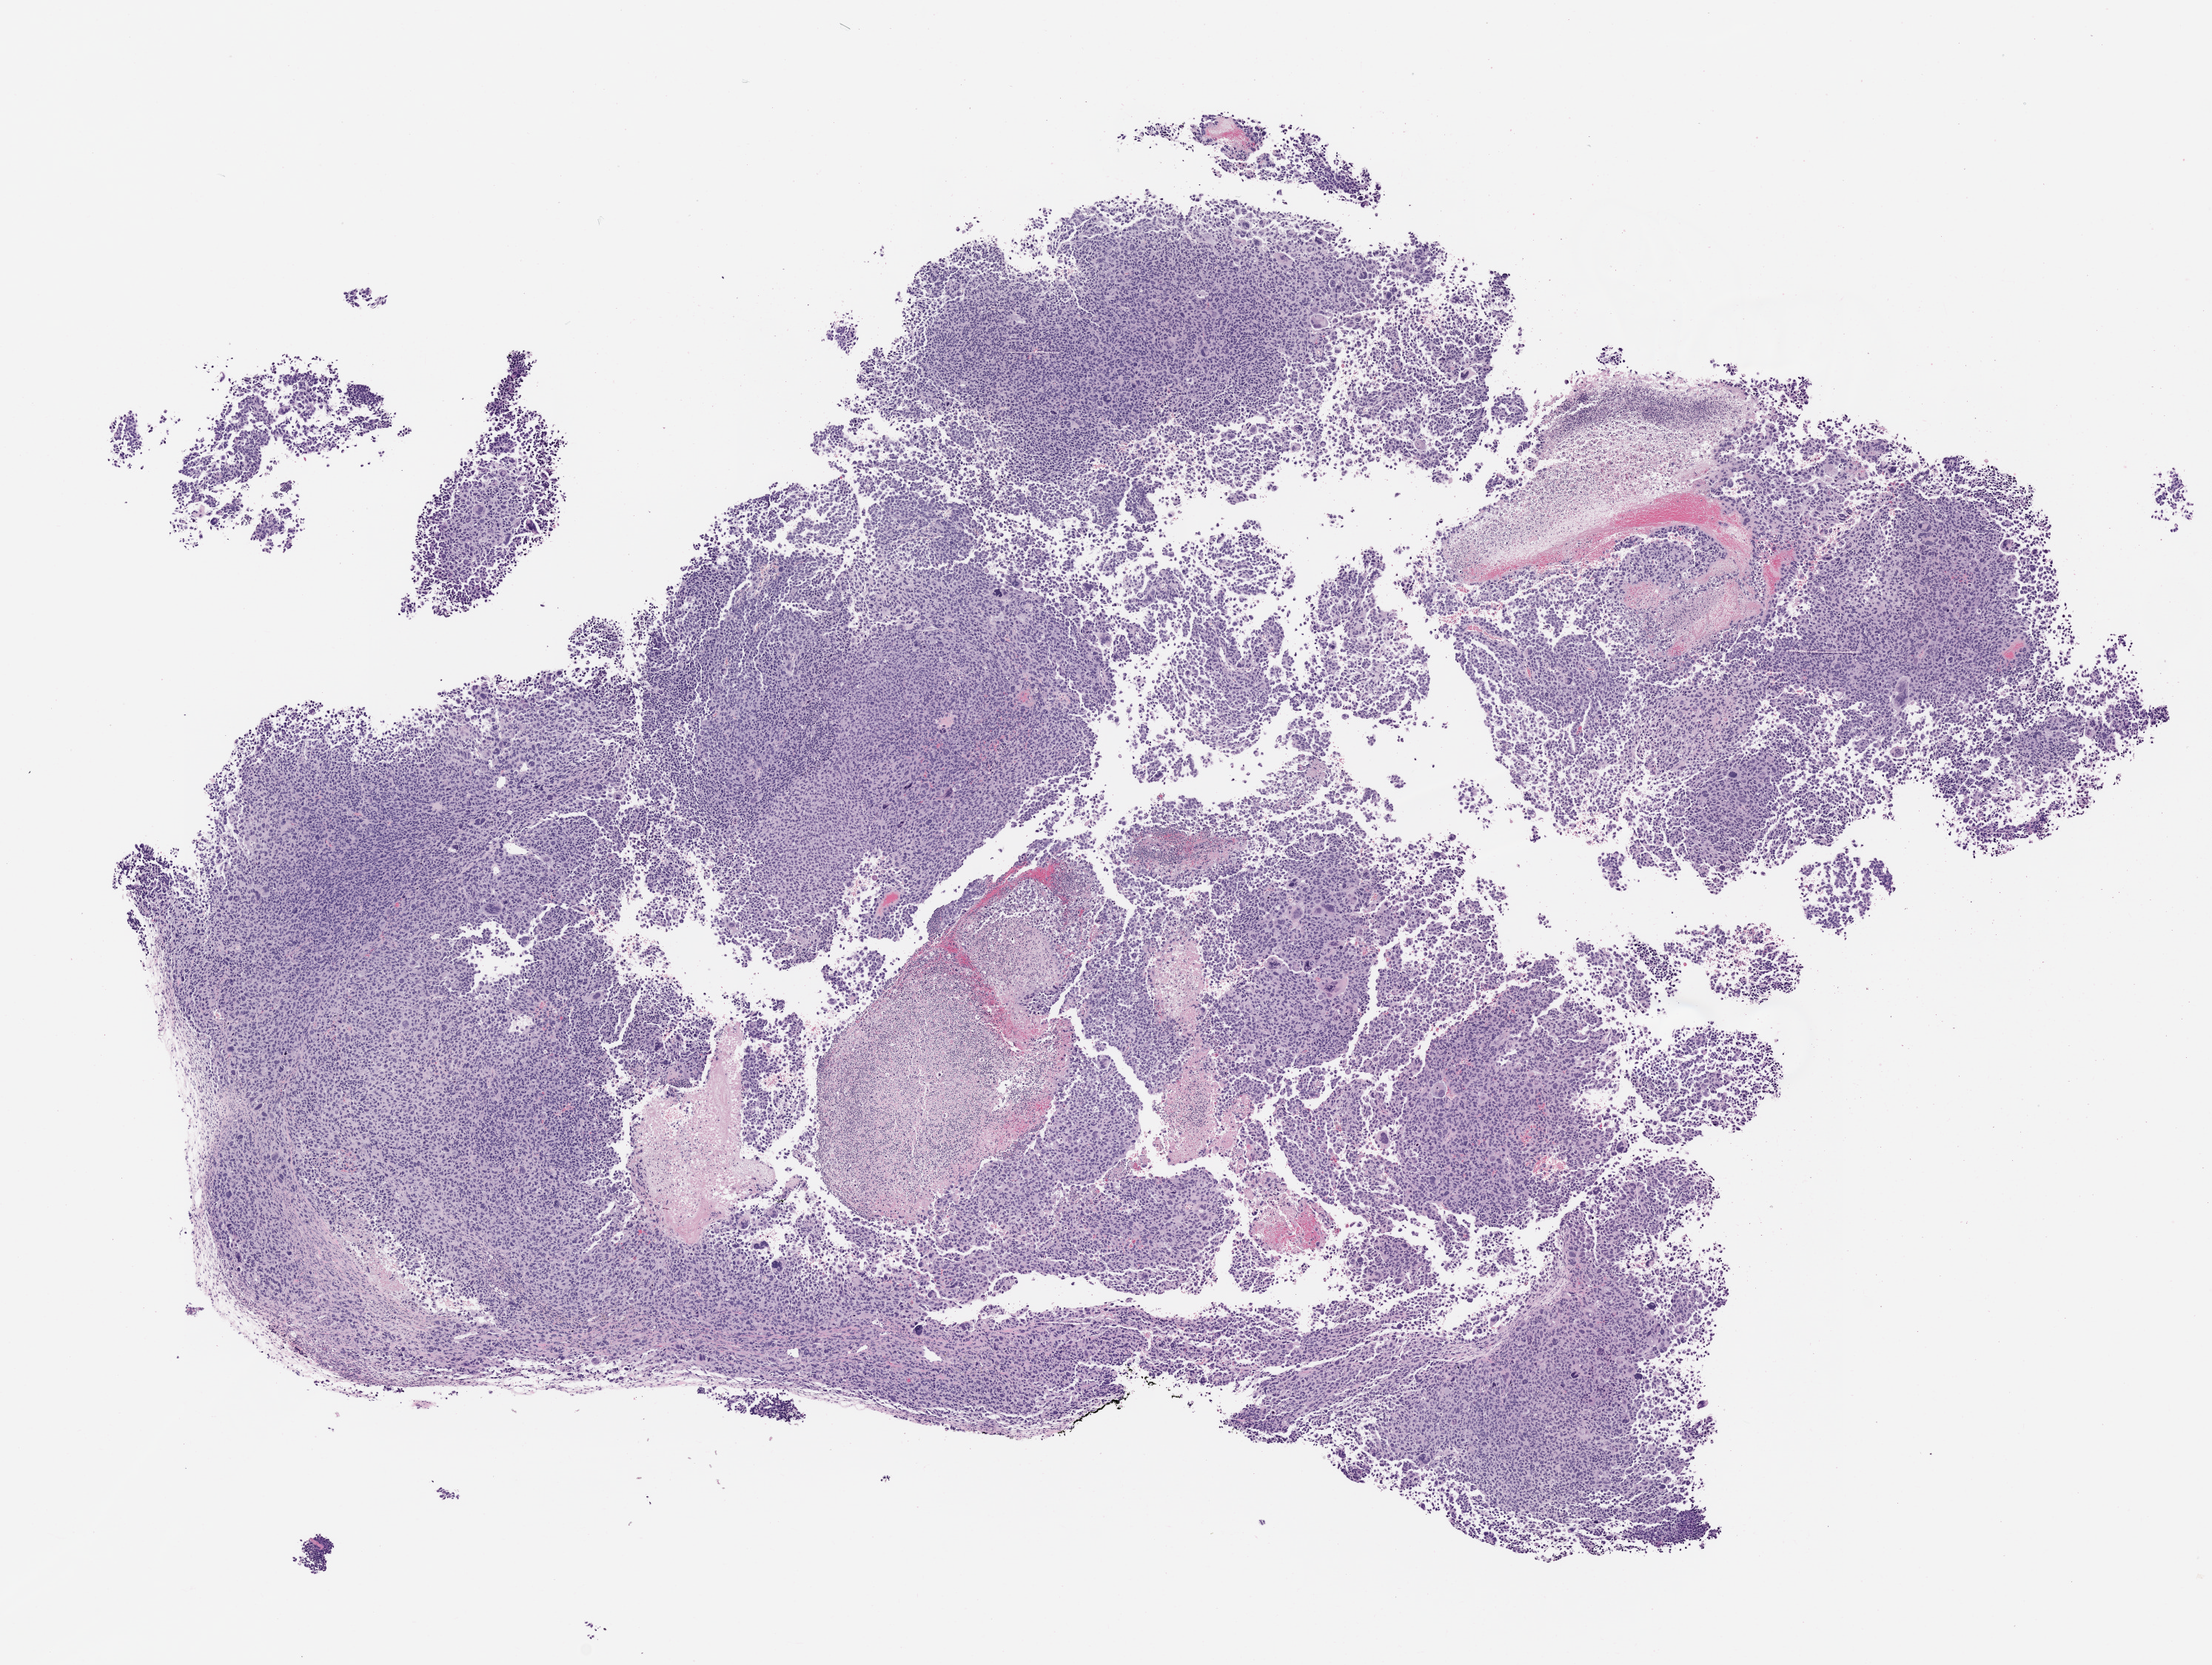
Haematoxylin and eosin whole-slide image of a patient-derived xenograft (PDX) tumor grown in a mouse, passage 1 — whole scanned area (about 12.0 x 9.0 mm) shown as a low-resolution overview, FFPE section, originating tumor site category: skin.
• originating patient diagnosis: Melanoma